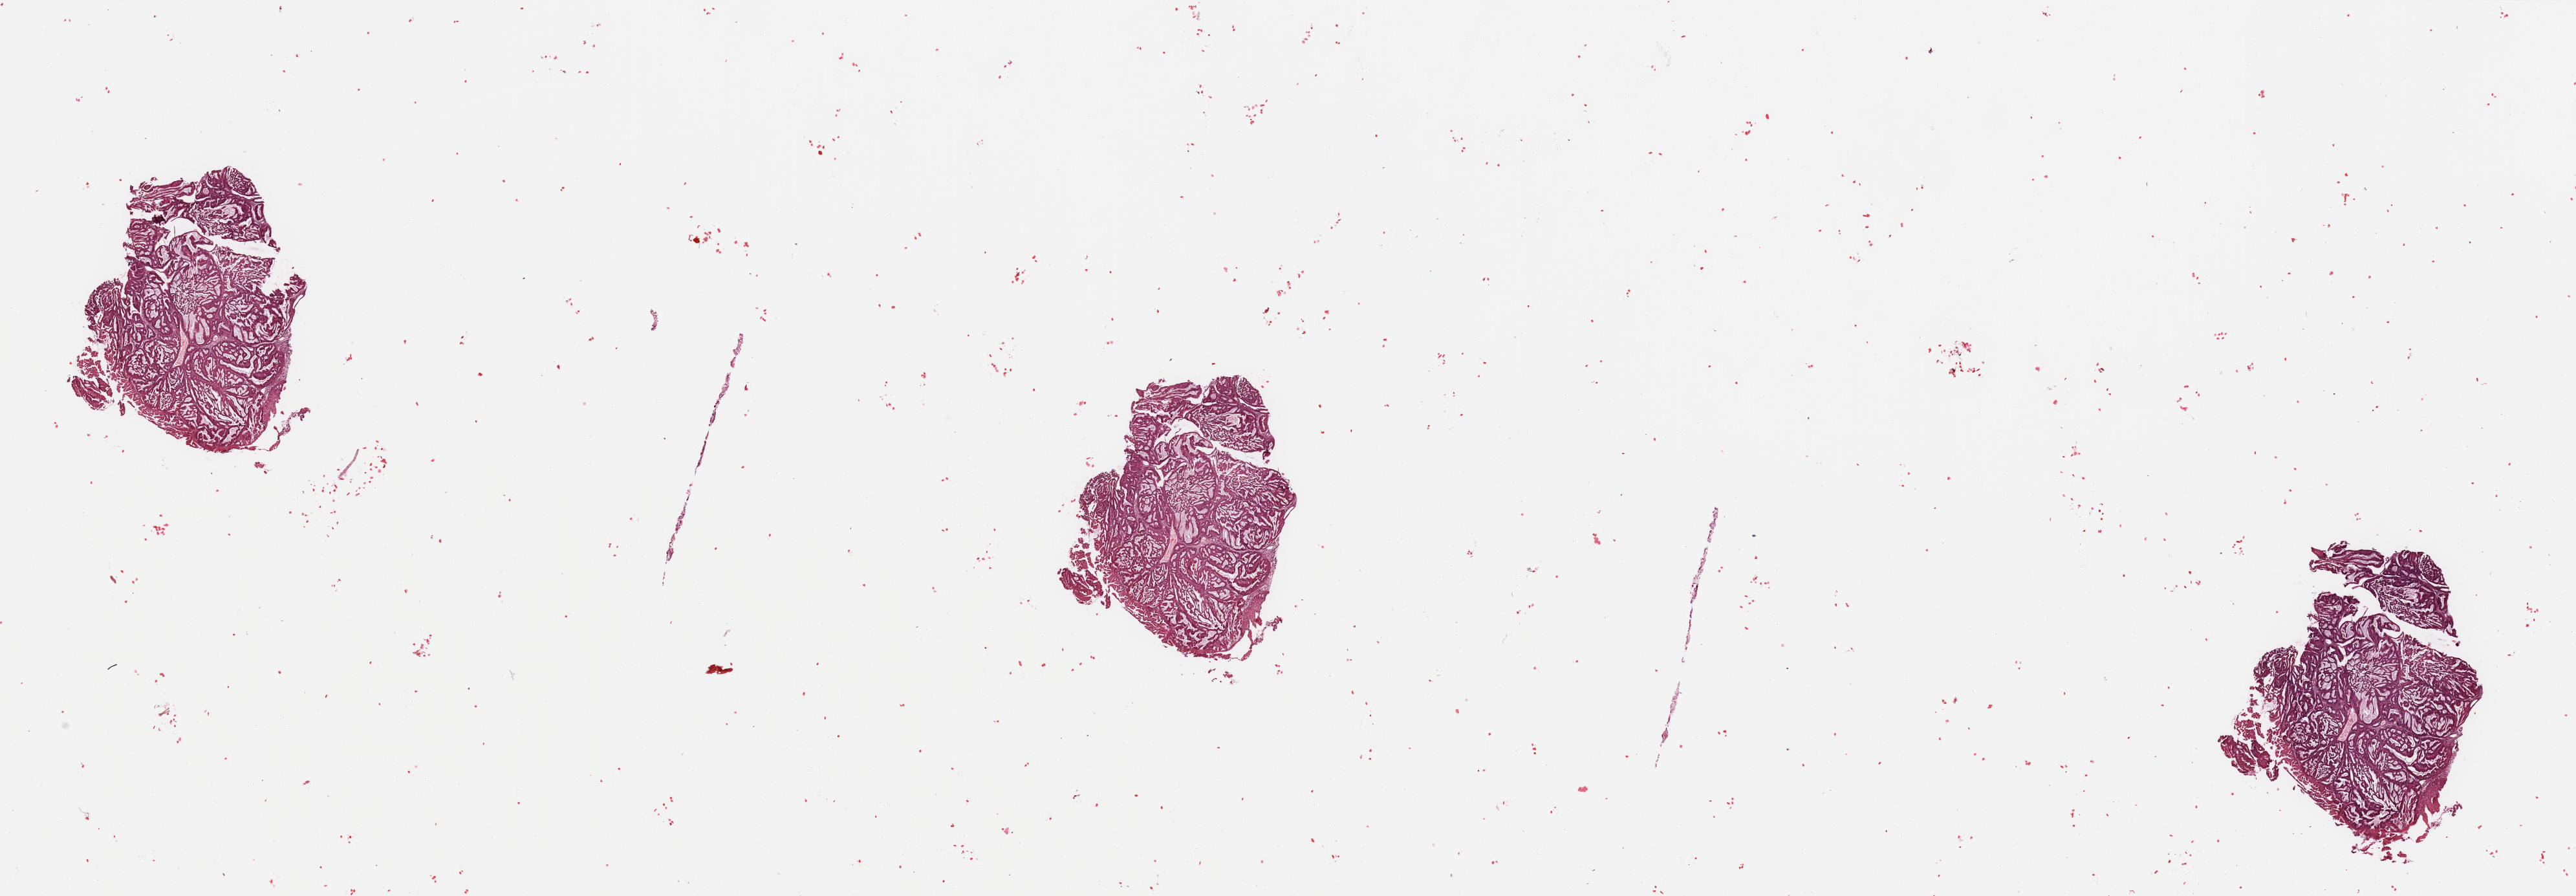
Hematoxylin and eosin (H&E) stained whole-slide image — a low-resolution overview of the entire scanned area, about 31.5 x 11.0 mm (from a 20x scan), tumour tissue sample, uterus. Patient: female, age 72 years.
- patient diagnosis (cohort enrolment): corpus endometrial carcinoma (uterus)
- primary tumour site (as recorded): posterior endometrium